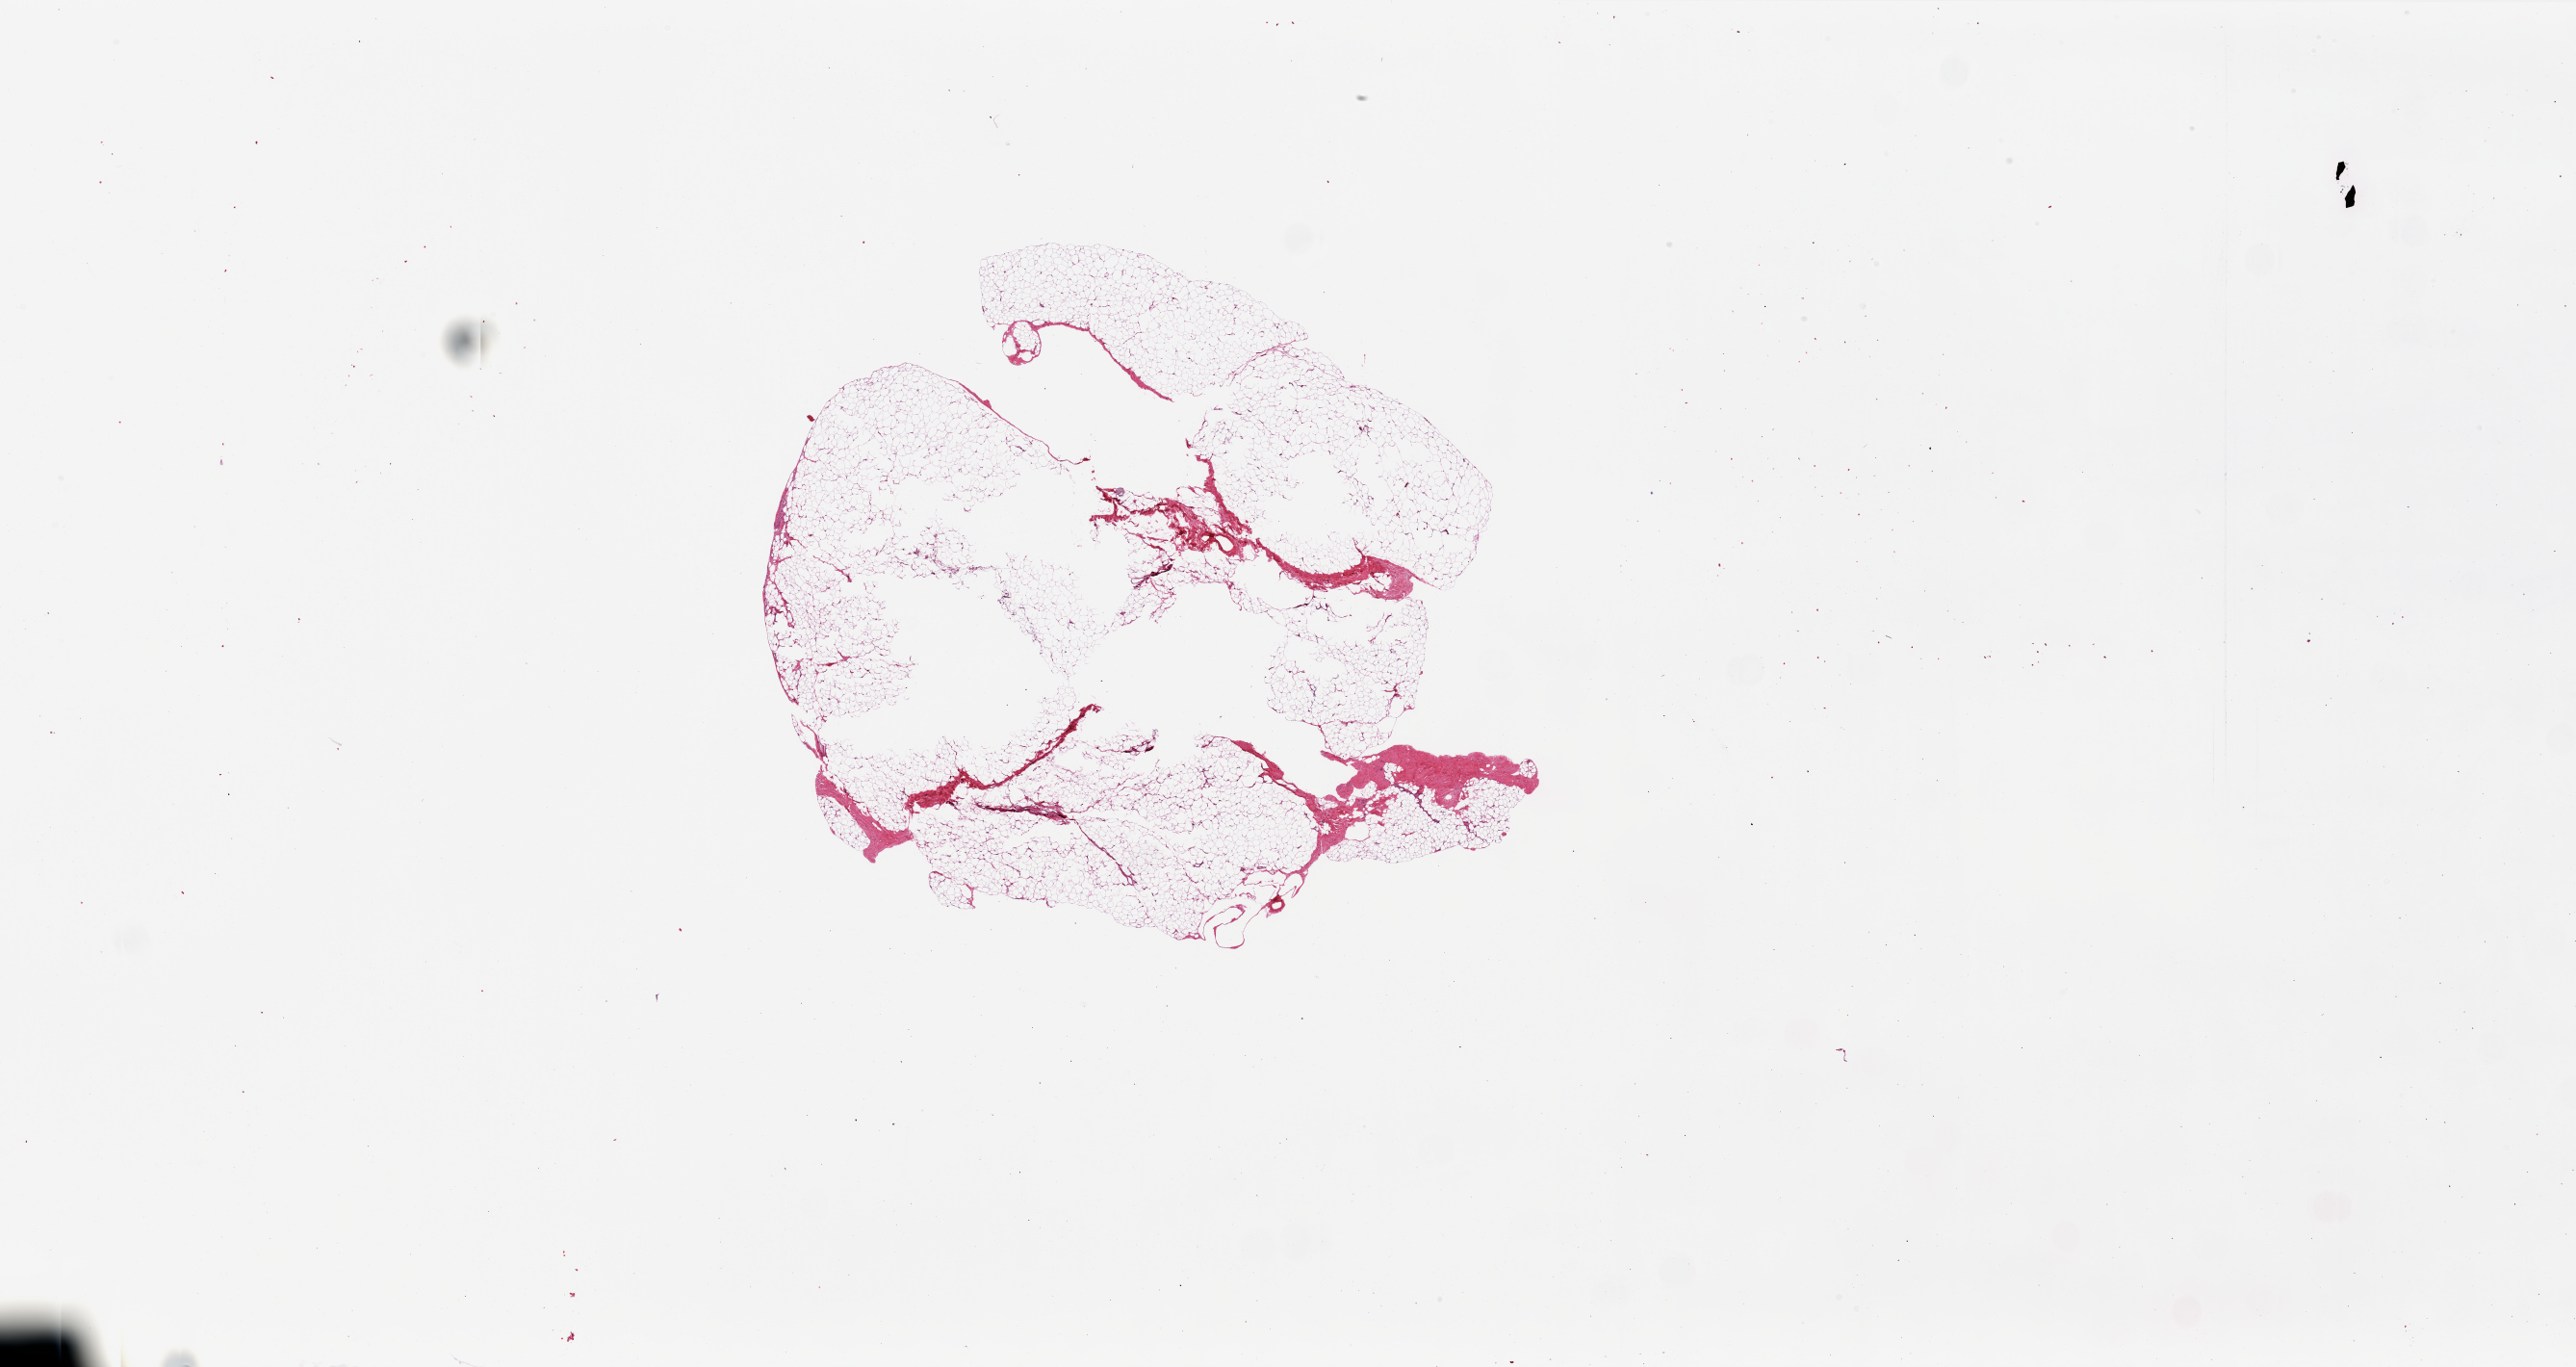
Hematoxylin and eosin (H&E) whole-slide image — low-resolution overview of the scanned area, about 42.3 x 22.5 mm (acquisition: 20x scan), PAXgene-fixed, paraffin-embedded tissue, target tissue: adipose tissue, tissue donor sample. Donor: male.
Review note (as recorded): center is unfixed.